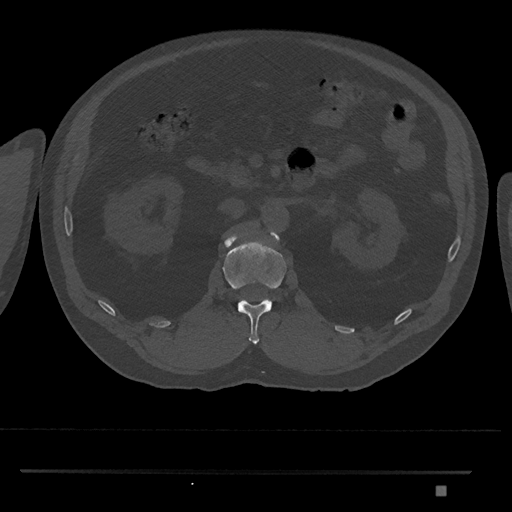
CT including the spine, one axial slice; slice 809 of 1134 in the series (ordered by position); reconstruction kernel Br40s/3; bone window (W 1800 / L 400 HU); 0.5 mm slice thickness; 512 × 512 image matrix, field of view 429 × 429 mm. Male patient, age 65 years. From the clinical record (not read from this slice): primary cancer: prostate.
Annotated regions visible in this slice (semi-automatic segmentation, software-assisted and operator-edited):
- L1 vertebra: box from (x=223, y=230) to (x=287, y=344) px